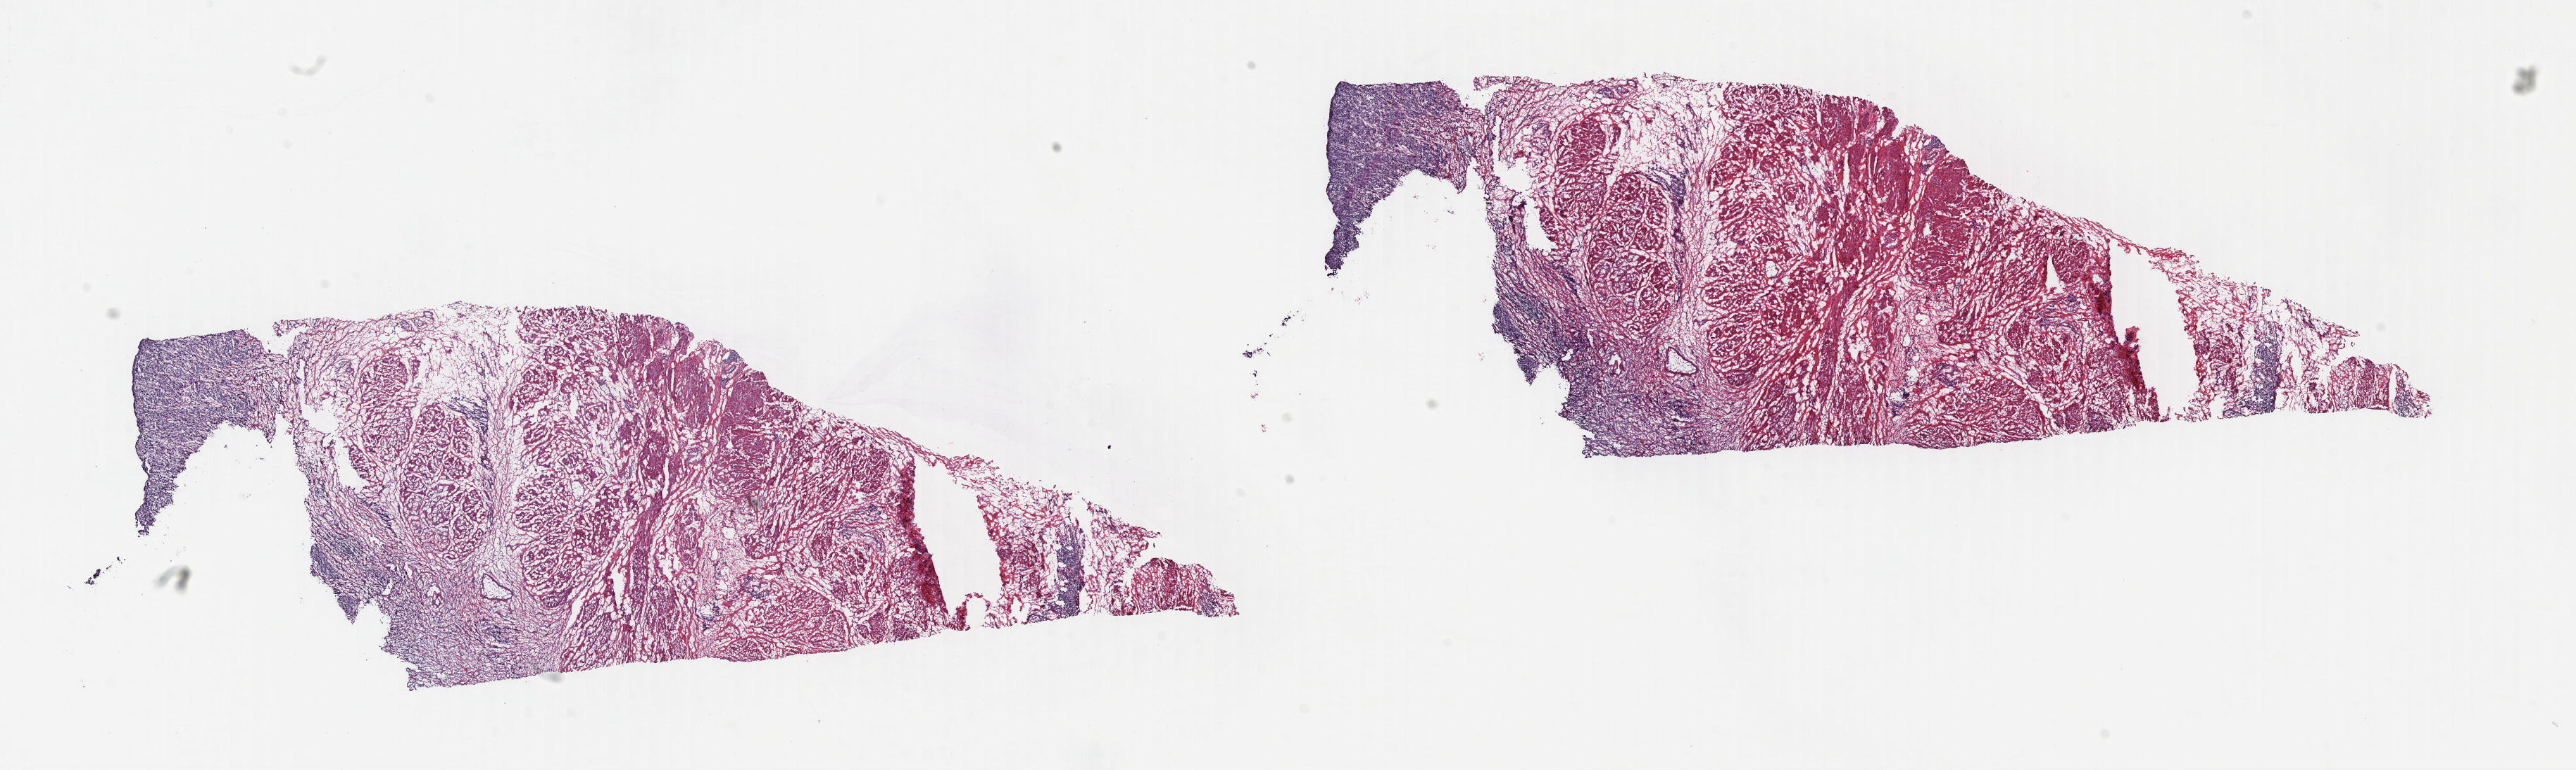
Digitized H&E tissue section (whole slide) — shown as a low-resolution overview of the whole scanned area (about 28.8 x 8.6 mm, slide scanned at 40x). Frozen section. Sample: primary tumour, bladder. Patient: male, age at initial diagnosis 57 years. Histologic grade: high grade. Pathologist review of this section (percent, as recorded): tumour cells 65%, tumour nuclei 65%, normal cells 0%, stromal cells 35%, necrosis 0%. Inflammatory infiltration, as recorded: lymphocyte infiltration 5%, monocyte infiltration 2%, neutrophil infiltration 3%.
• TNM: T2b N0 MX
• AJCC pathologic stage: II (7th edition)
• lymph nodes positive (case pathology): 0 of 34 examined
• pathologic diagnosis: Transitional cell carcinoma (lateral wall of bladder)